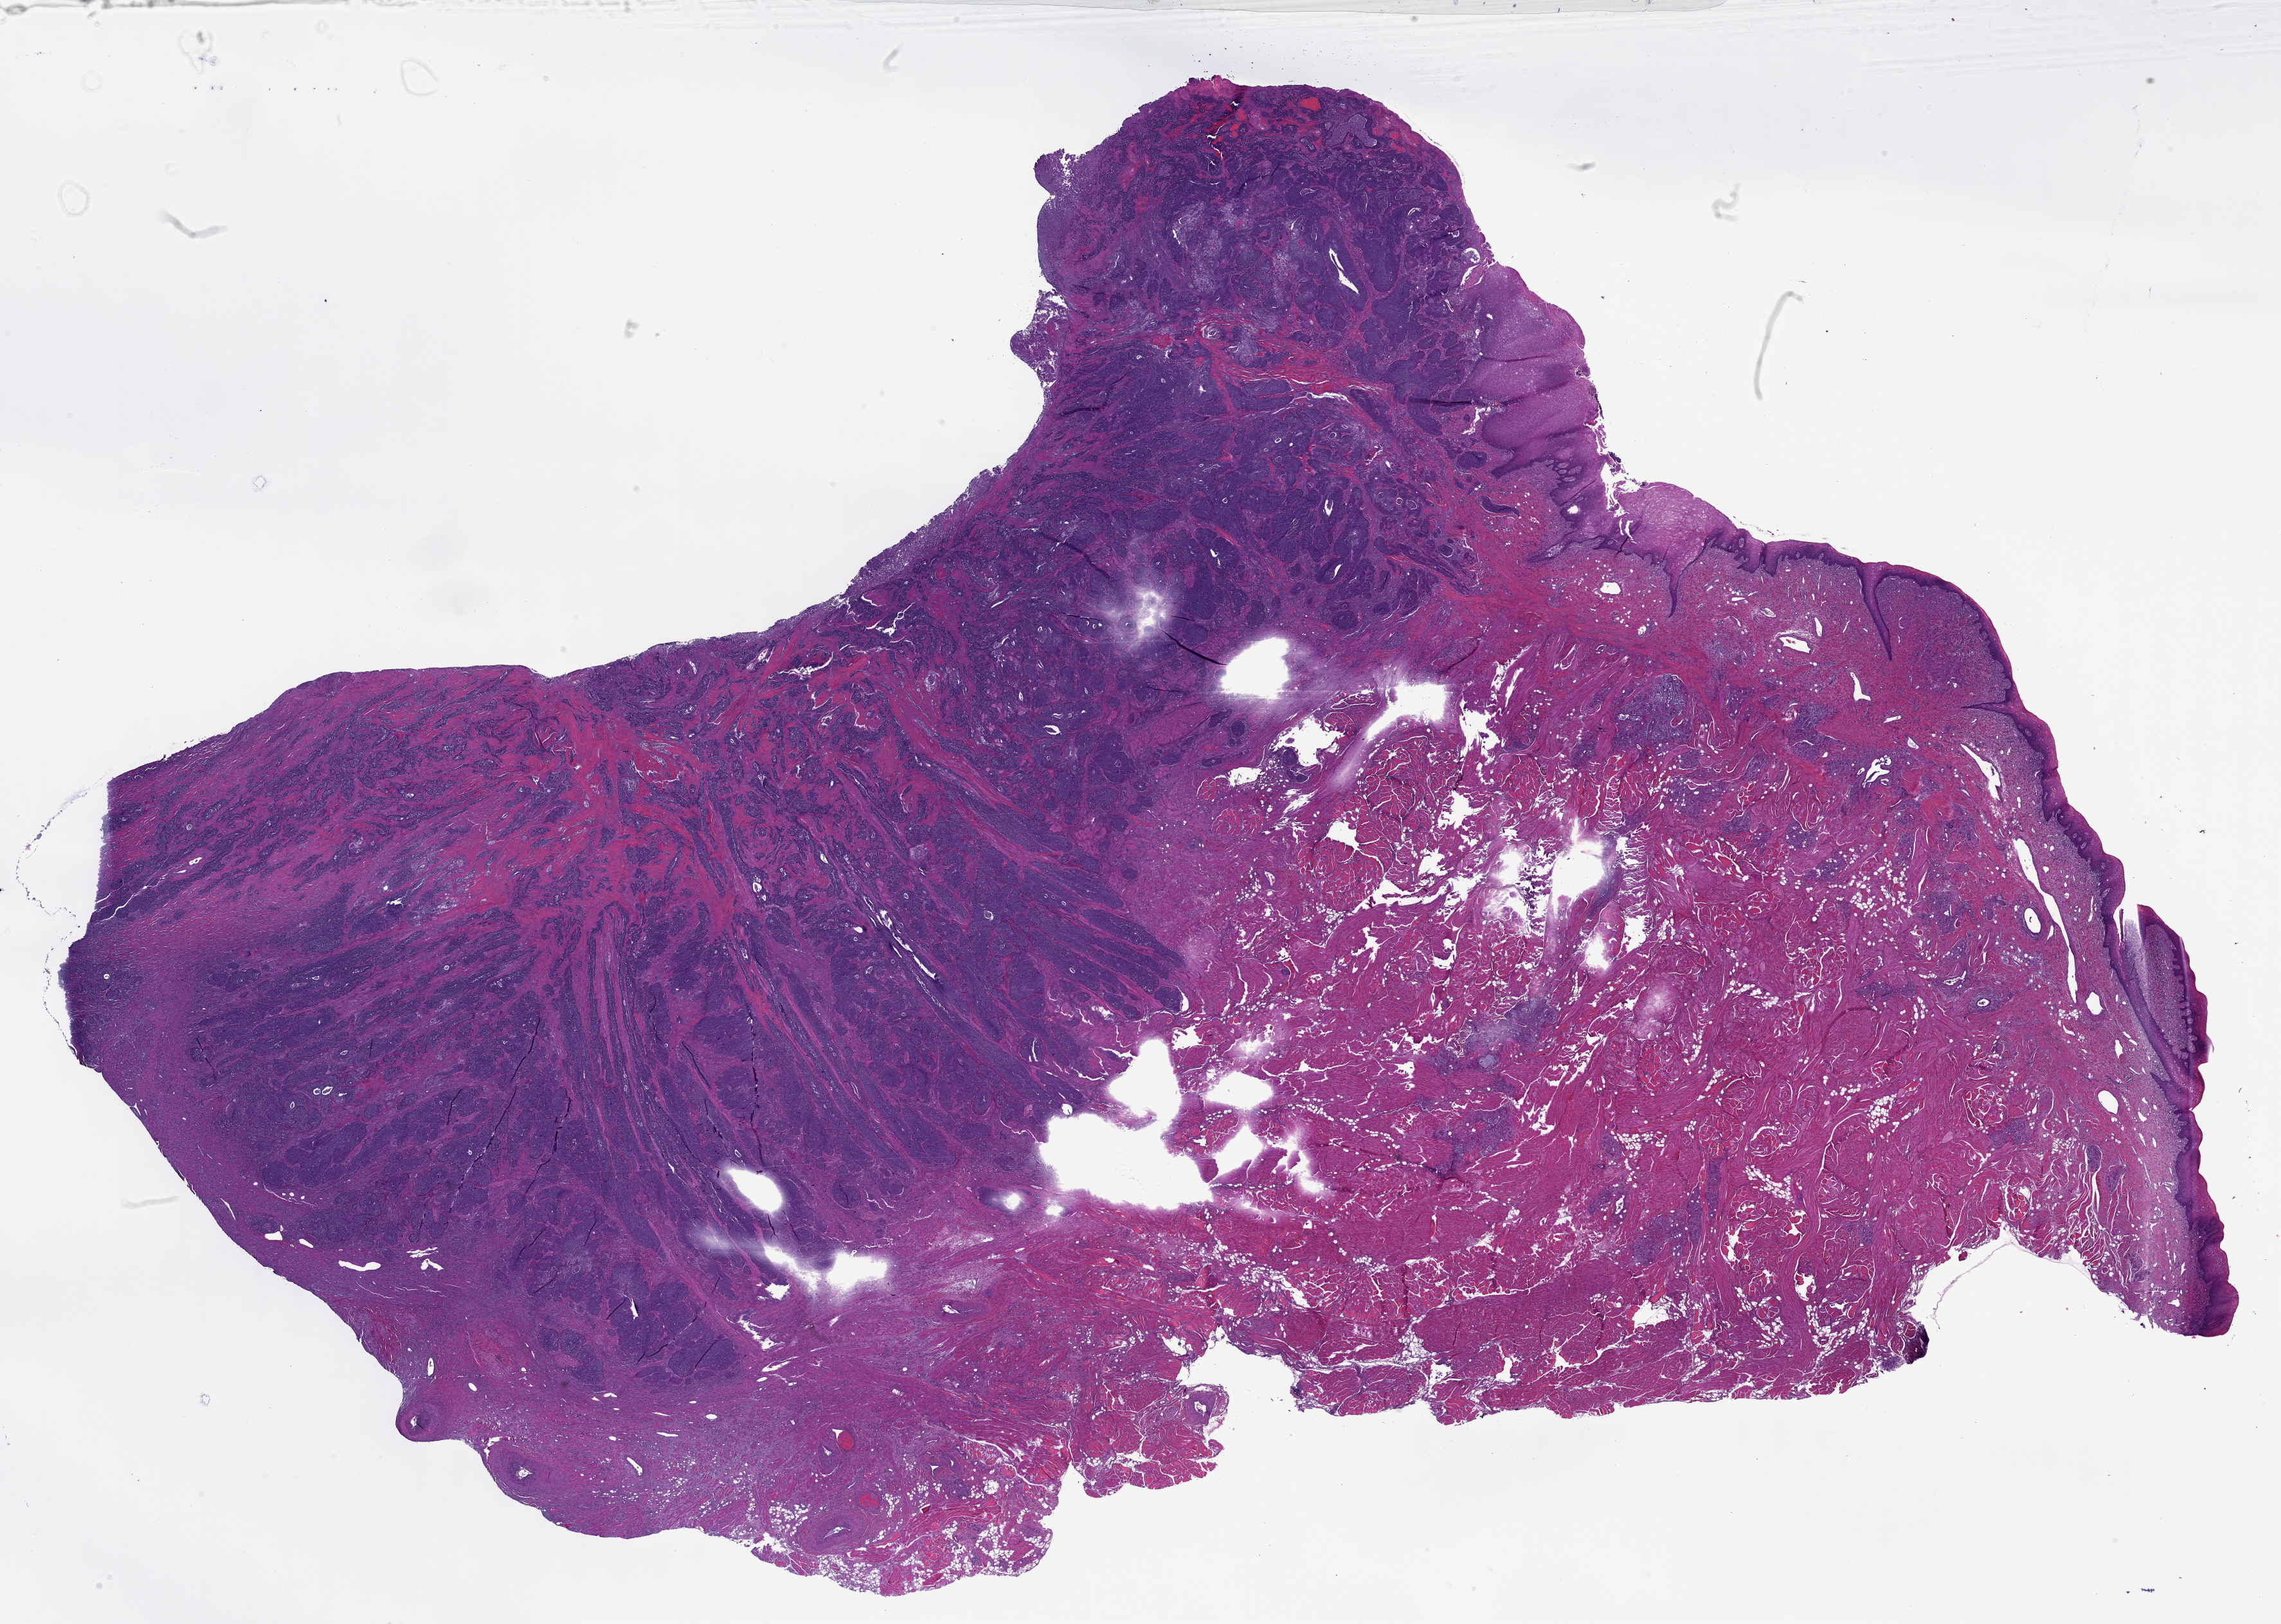
Digitized H&E tissue section (whole slide) — a low-resolution overview of the entire scanned area, about 28.7 x 20.4 mm (slide scanned at 40x); formalin-fixed paraffin-embedded (FFPE) diagnostic section; primary tumour sample from the head and neck. Male, age 60 years at initial diagnosis. Histologic grade: G3 (poorly differentiated).
AJCC pathologic stage: III (7th edition). Pathologic diagnosis: Squamous cell carcinoma, NOS.